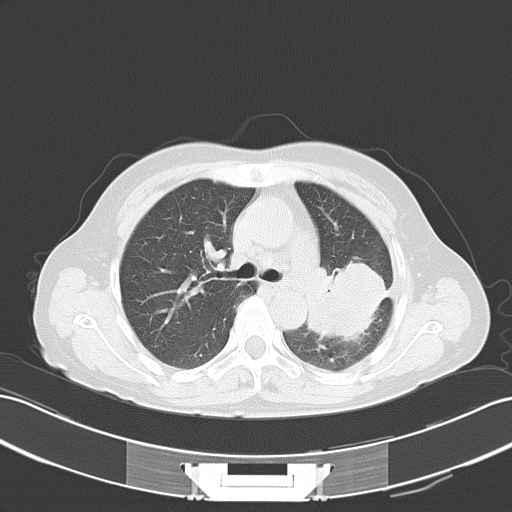
Chest CT, one axial slice; slice 33 of 51 in the series (ordered by position); 120 kVp; lung window (W 1500 / L -600 HU); 512 × 512 image matrix, field of view 353 × 353 mm. Female patient, age 54 years. Case-level facts recorded for this patient, not image findings: clinical TNM (as recorded): T3 N1 M0.
Annotated regions visible in this slice (rectangle marked by the reading radiologist):
- lung tumour (recorded histology: adenocarcinoma): box from (x=305, y=254) to (x=391, y=350) px